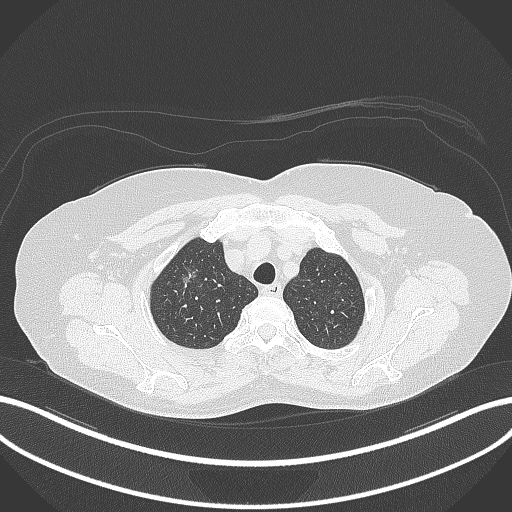
Chest CT, one axial slice. Position 297 of 365 along the scan axis. Reconstruction kernel B70f. 120 kVp. Lung window (W 1500 / L -600 HU). 1 mm slice thickness. 512 × 512 image matrix, field of view 400 × 400 mm. Female patient, age 62 years. From the clinical record (not read from this slice): clinical TNM (as recorded): T1c N0 M0.
Structures marked on this image (rectangle marked by the reading radiologist):
- lung tumour (recorded histology: adenocarcinoma): bounding box [x1, y1, x2, y2] px = [176, 255, 206, 288]